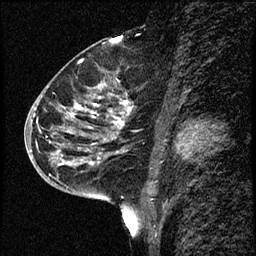
Breast MRI (dynamic contrast-enhanced), one sagittal slice; slice 34 of 68 in the series (ordered by position); dynamic contrast-enhanced study with each time point stored as its own series, time point 2 of 3 at this slice position (early post-contrast, ordered by acquisition time); 1.5 T; TE 4.2 ms, TR 17.6 ms; 2 mm slice thickness; 256 × 256 image matrix, field of view 200 × 200 mm. Female patient, age 52 years. From the clinical record (not read from this slice): setting: breast cancer imaged before/during neoadjuvant chemotherapy; receptor status: HER2-positive.
Structures marked on this image (semi-automatic segmentation, software-assisted and operator-edited):
- analysis volume of interest (the breast-tissue region the enhancement analysis was run in; not a lesion): box from (x=50, y=61) to (x=132, y=184) px
- tumour enhancement mask (voxels above the 100 % enhancement threshold inside the analysis volume of interest): (x=57, y=85)–(x=129, y=164)